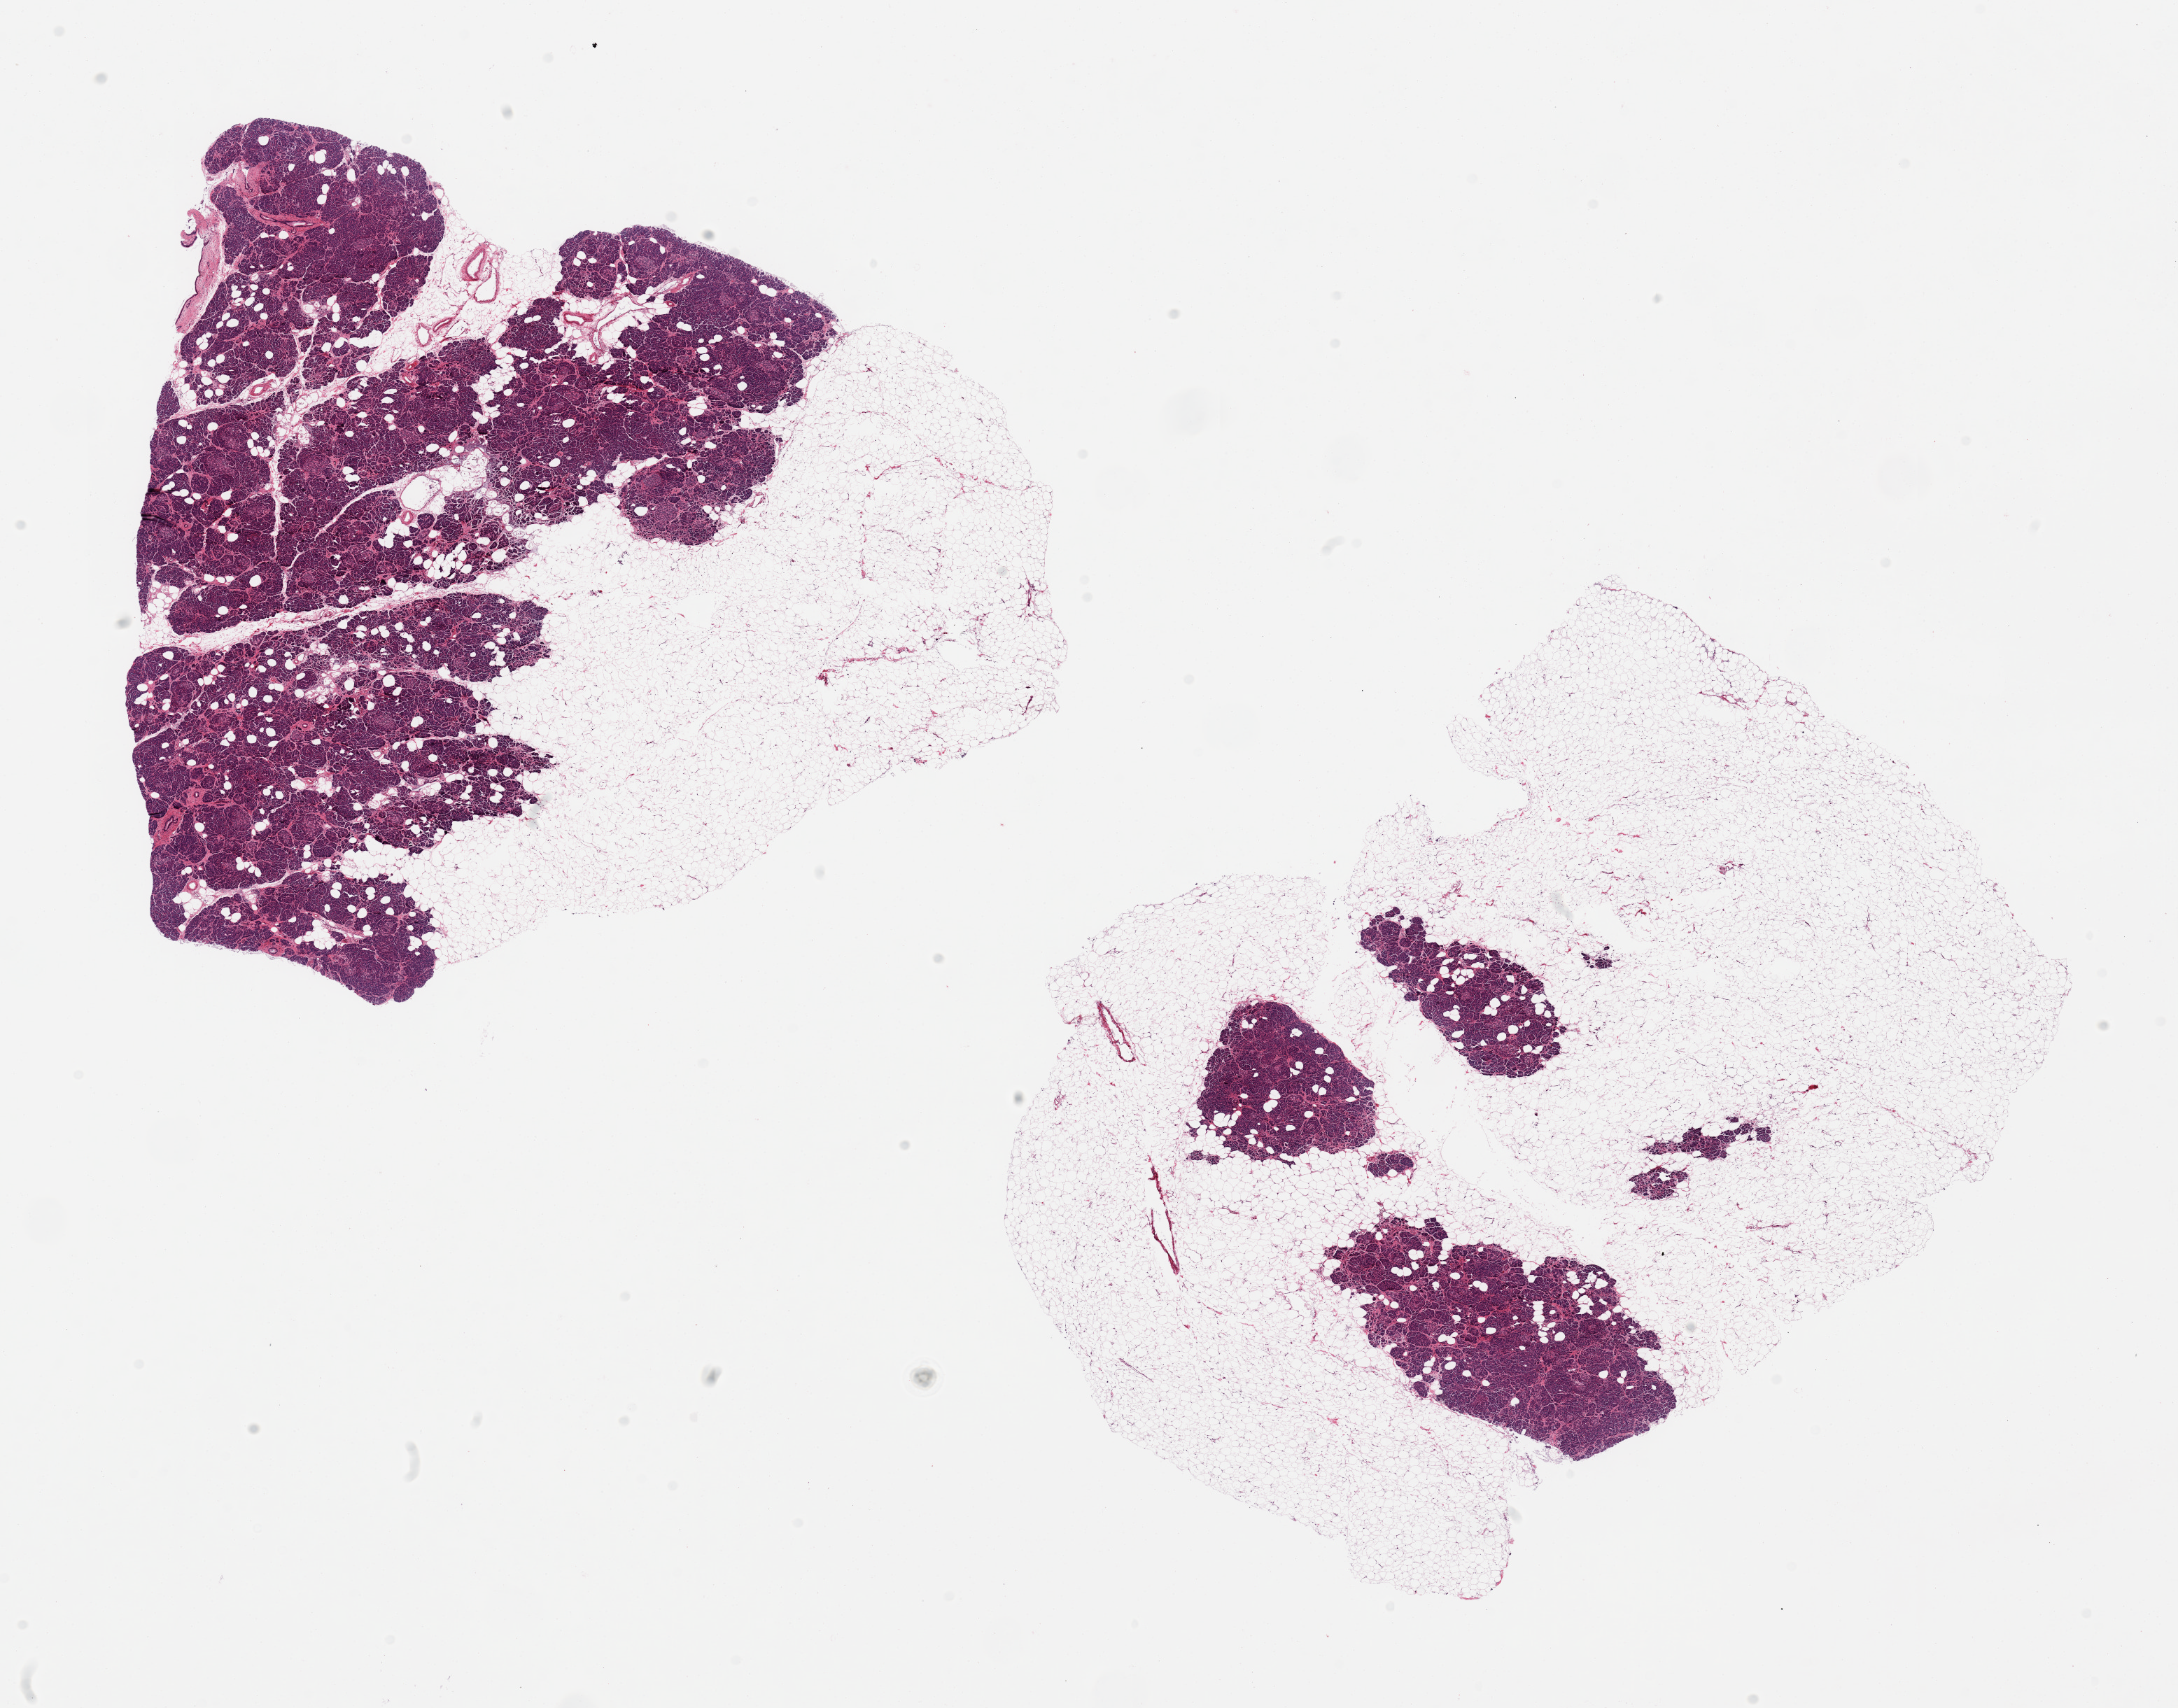
H&E whole-slide image, brightfield, a low-resolution overview of the entire scanned area, about 24.6 x 19.3 mm (slide scanned at 20x), PAXgene-fixed paraffin-embedded (PFPE) section, target tissue: pancreas, donor tissue sample. Female donor.
* reviewer comment on this tissue sample: 2 pieces; 1 piece has 80% internal and external fat; other has 40%; islets well formed in size and number